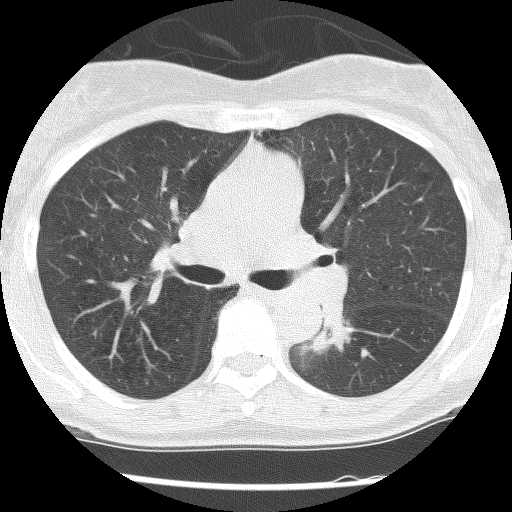
Chest CT (low-dose screening protocol), one axial image. Second annual screen. Lung window (W 1500 / L -600 HU). 2.5 mm slice thickness. Lung (sharp) reconstruction kernel (BONE). Slice 49 of 120 in the series. 512 × 512 image matrix, field of view 290 × 290 mm. Female, age 62 years at enrolment. Former smoker at enrolment.
Lesion marked by an expert reader, bounding box <298,308,351,355> (left, top, right, bottom; pixels). Reader record for this screening exam (exam-level; its link to the box is not recorded): non-calcified nodule or mass ≥4 mm, right upper lobe, 30 × 30 mm, poorly defined margins, ground glass attenuation, pre-existing on the prior screen: yes; interval growth: no. Note: the box lies in the patient's left hemithorax on this image, whereas the reader's record names the right lung; they may be different findings. Lung cancer was diagnosed 584 days after this screen: squamous cell carcinoma, NOS, left lower lobe, stage IIIB (AJCC 6th edition), 31 mm at pathology.